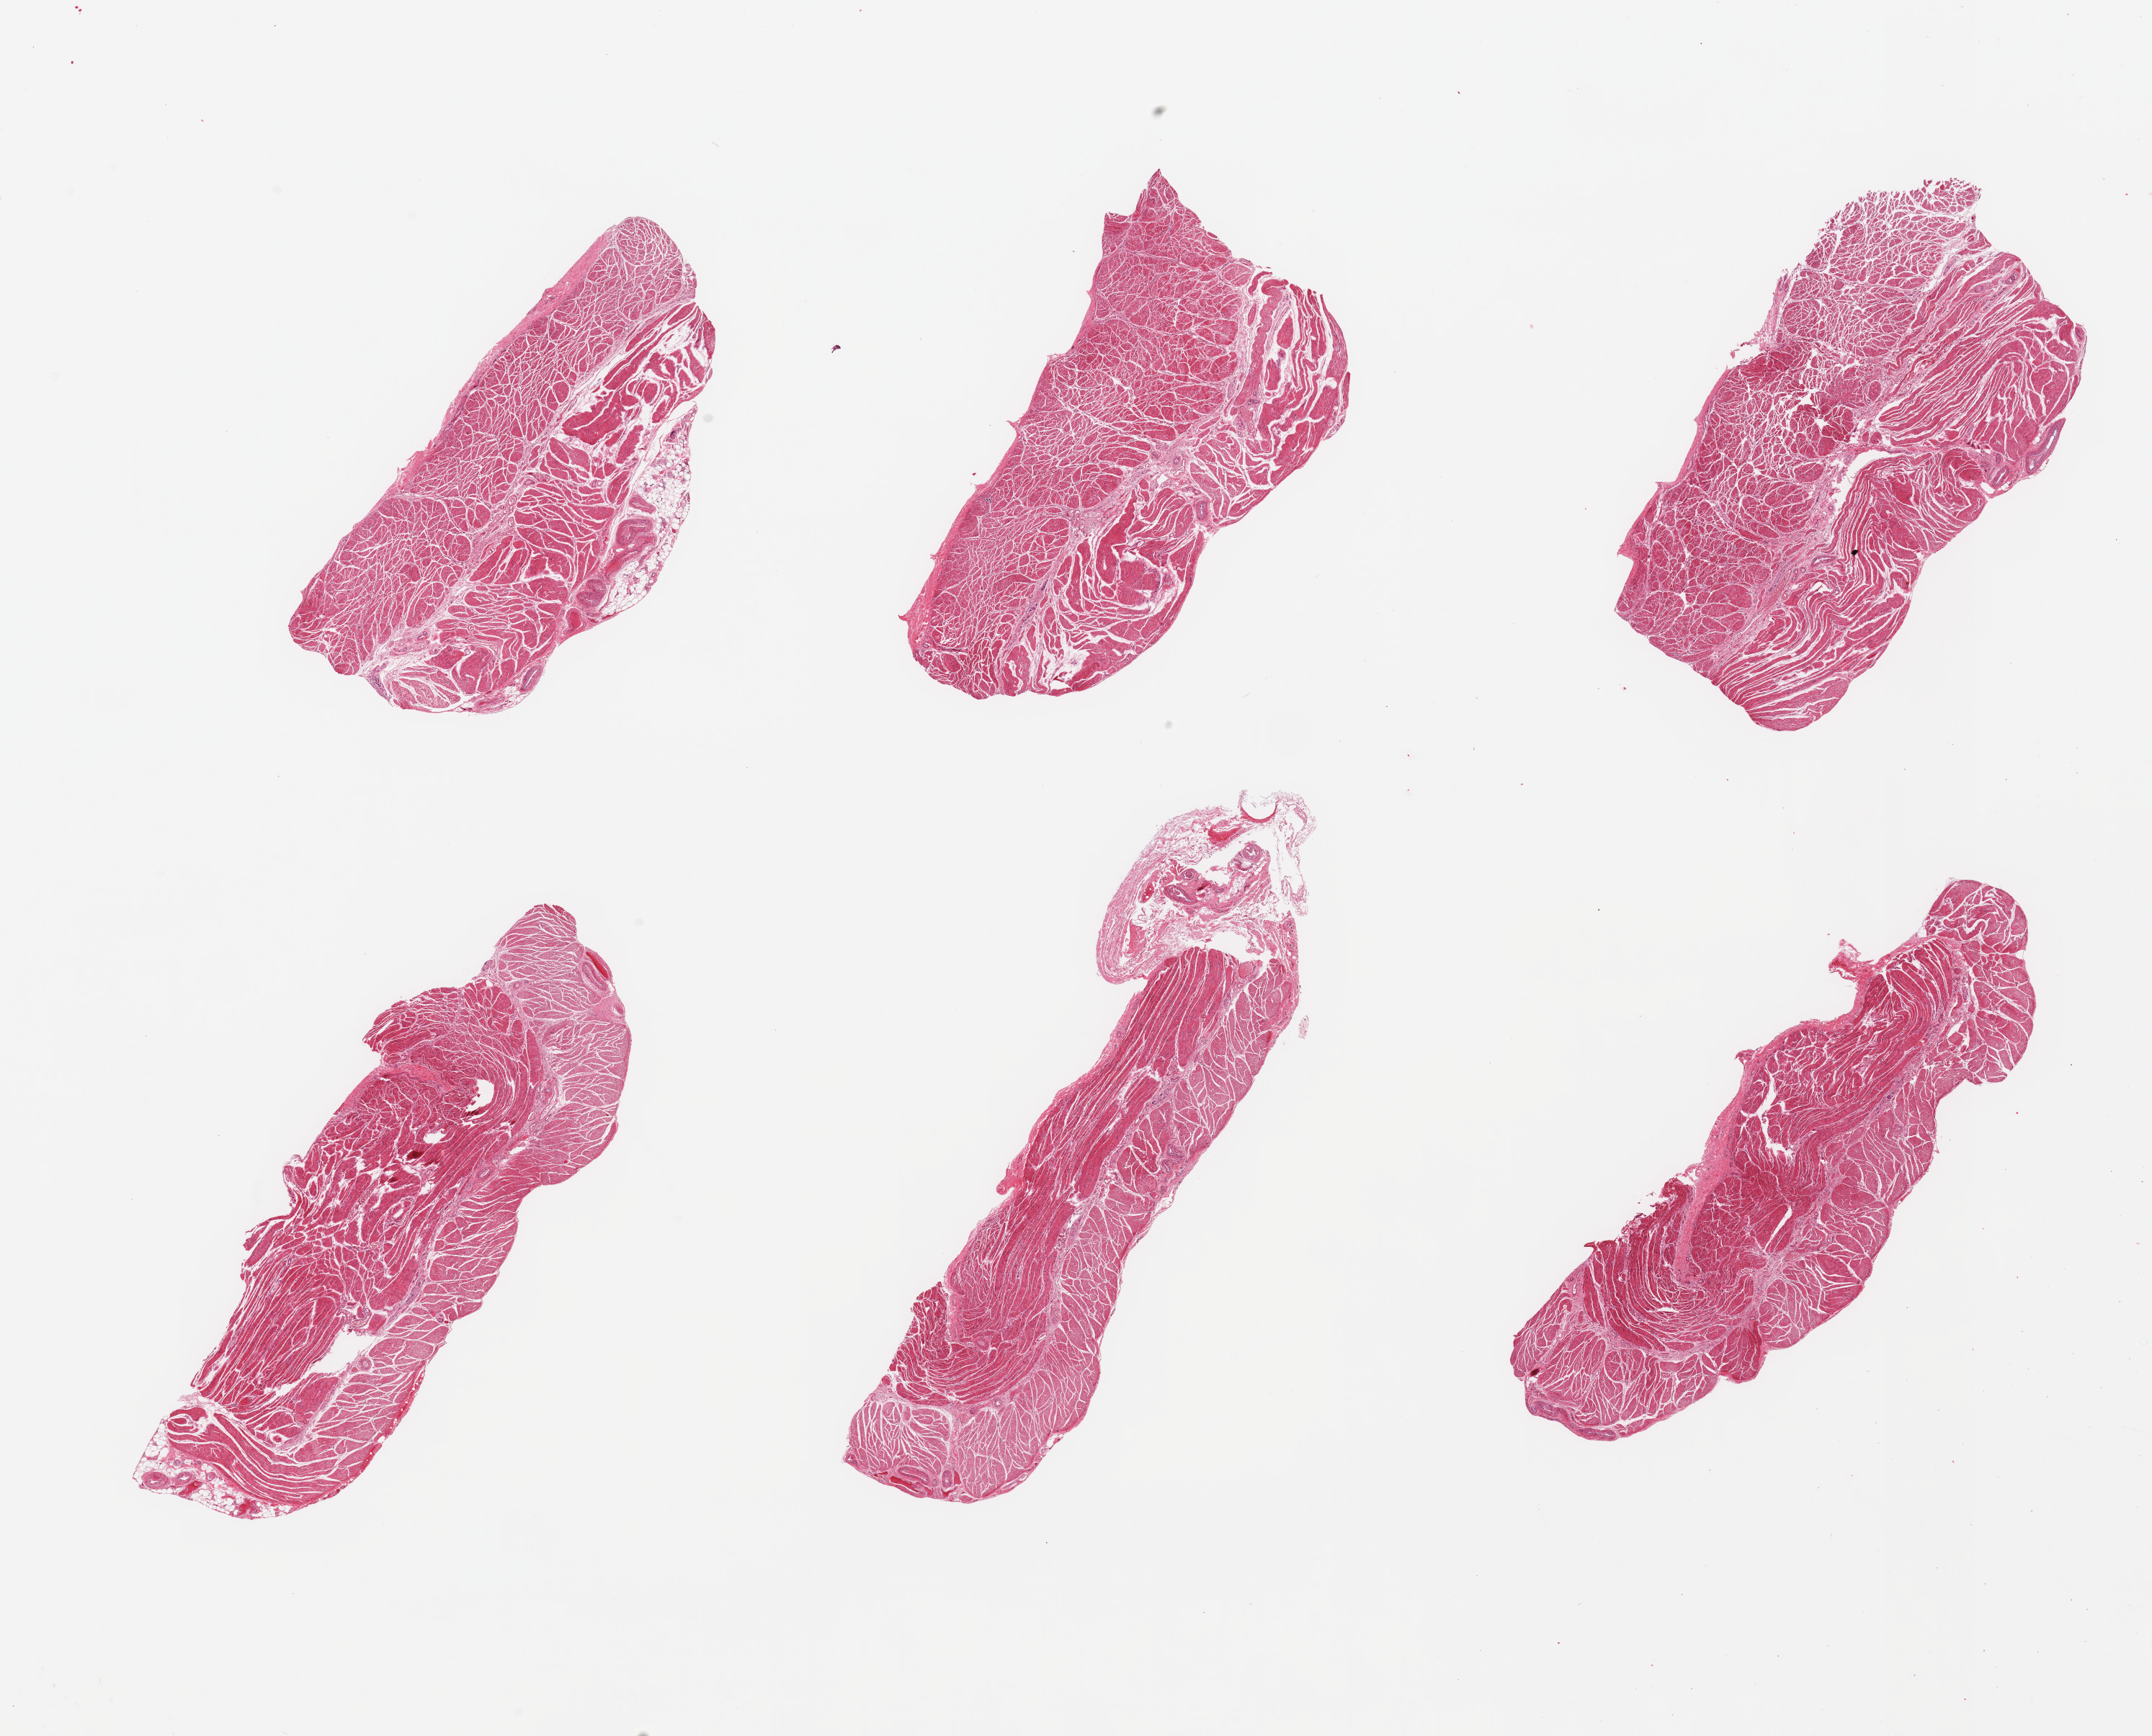
Digitized hematoxylin and eosin (H&E)-stained section, brightfield, shown as a low-resolution overview of the whole scanned area (about 23.6 x 19.1 mm); PAXgene-fixed, paraffin-embedded tissue; sampled site (target tissue): gastroesophageal junction; donor tissue sample. Donor sex: male.
Reviewer comment on this tissue sample: 6 pieces; well trimmed muscle except for 2.8mm labeled stromal focus on edge of 1 piece.